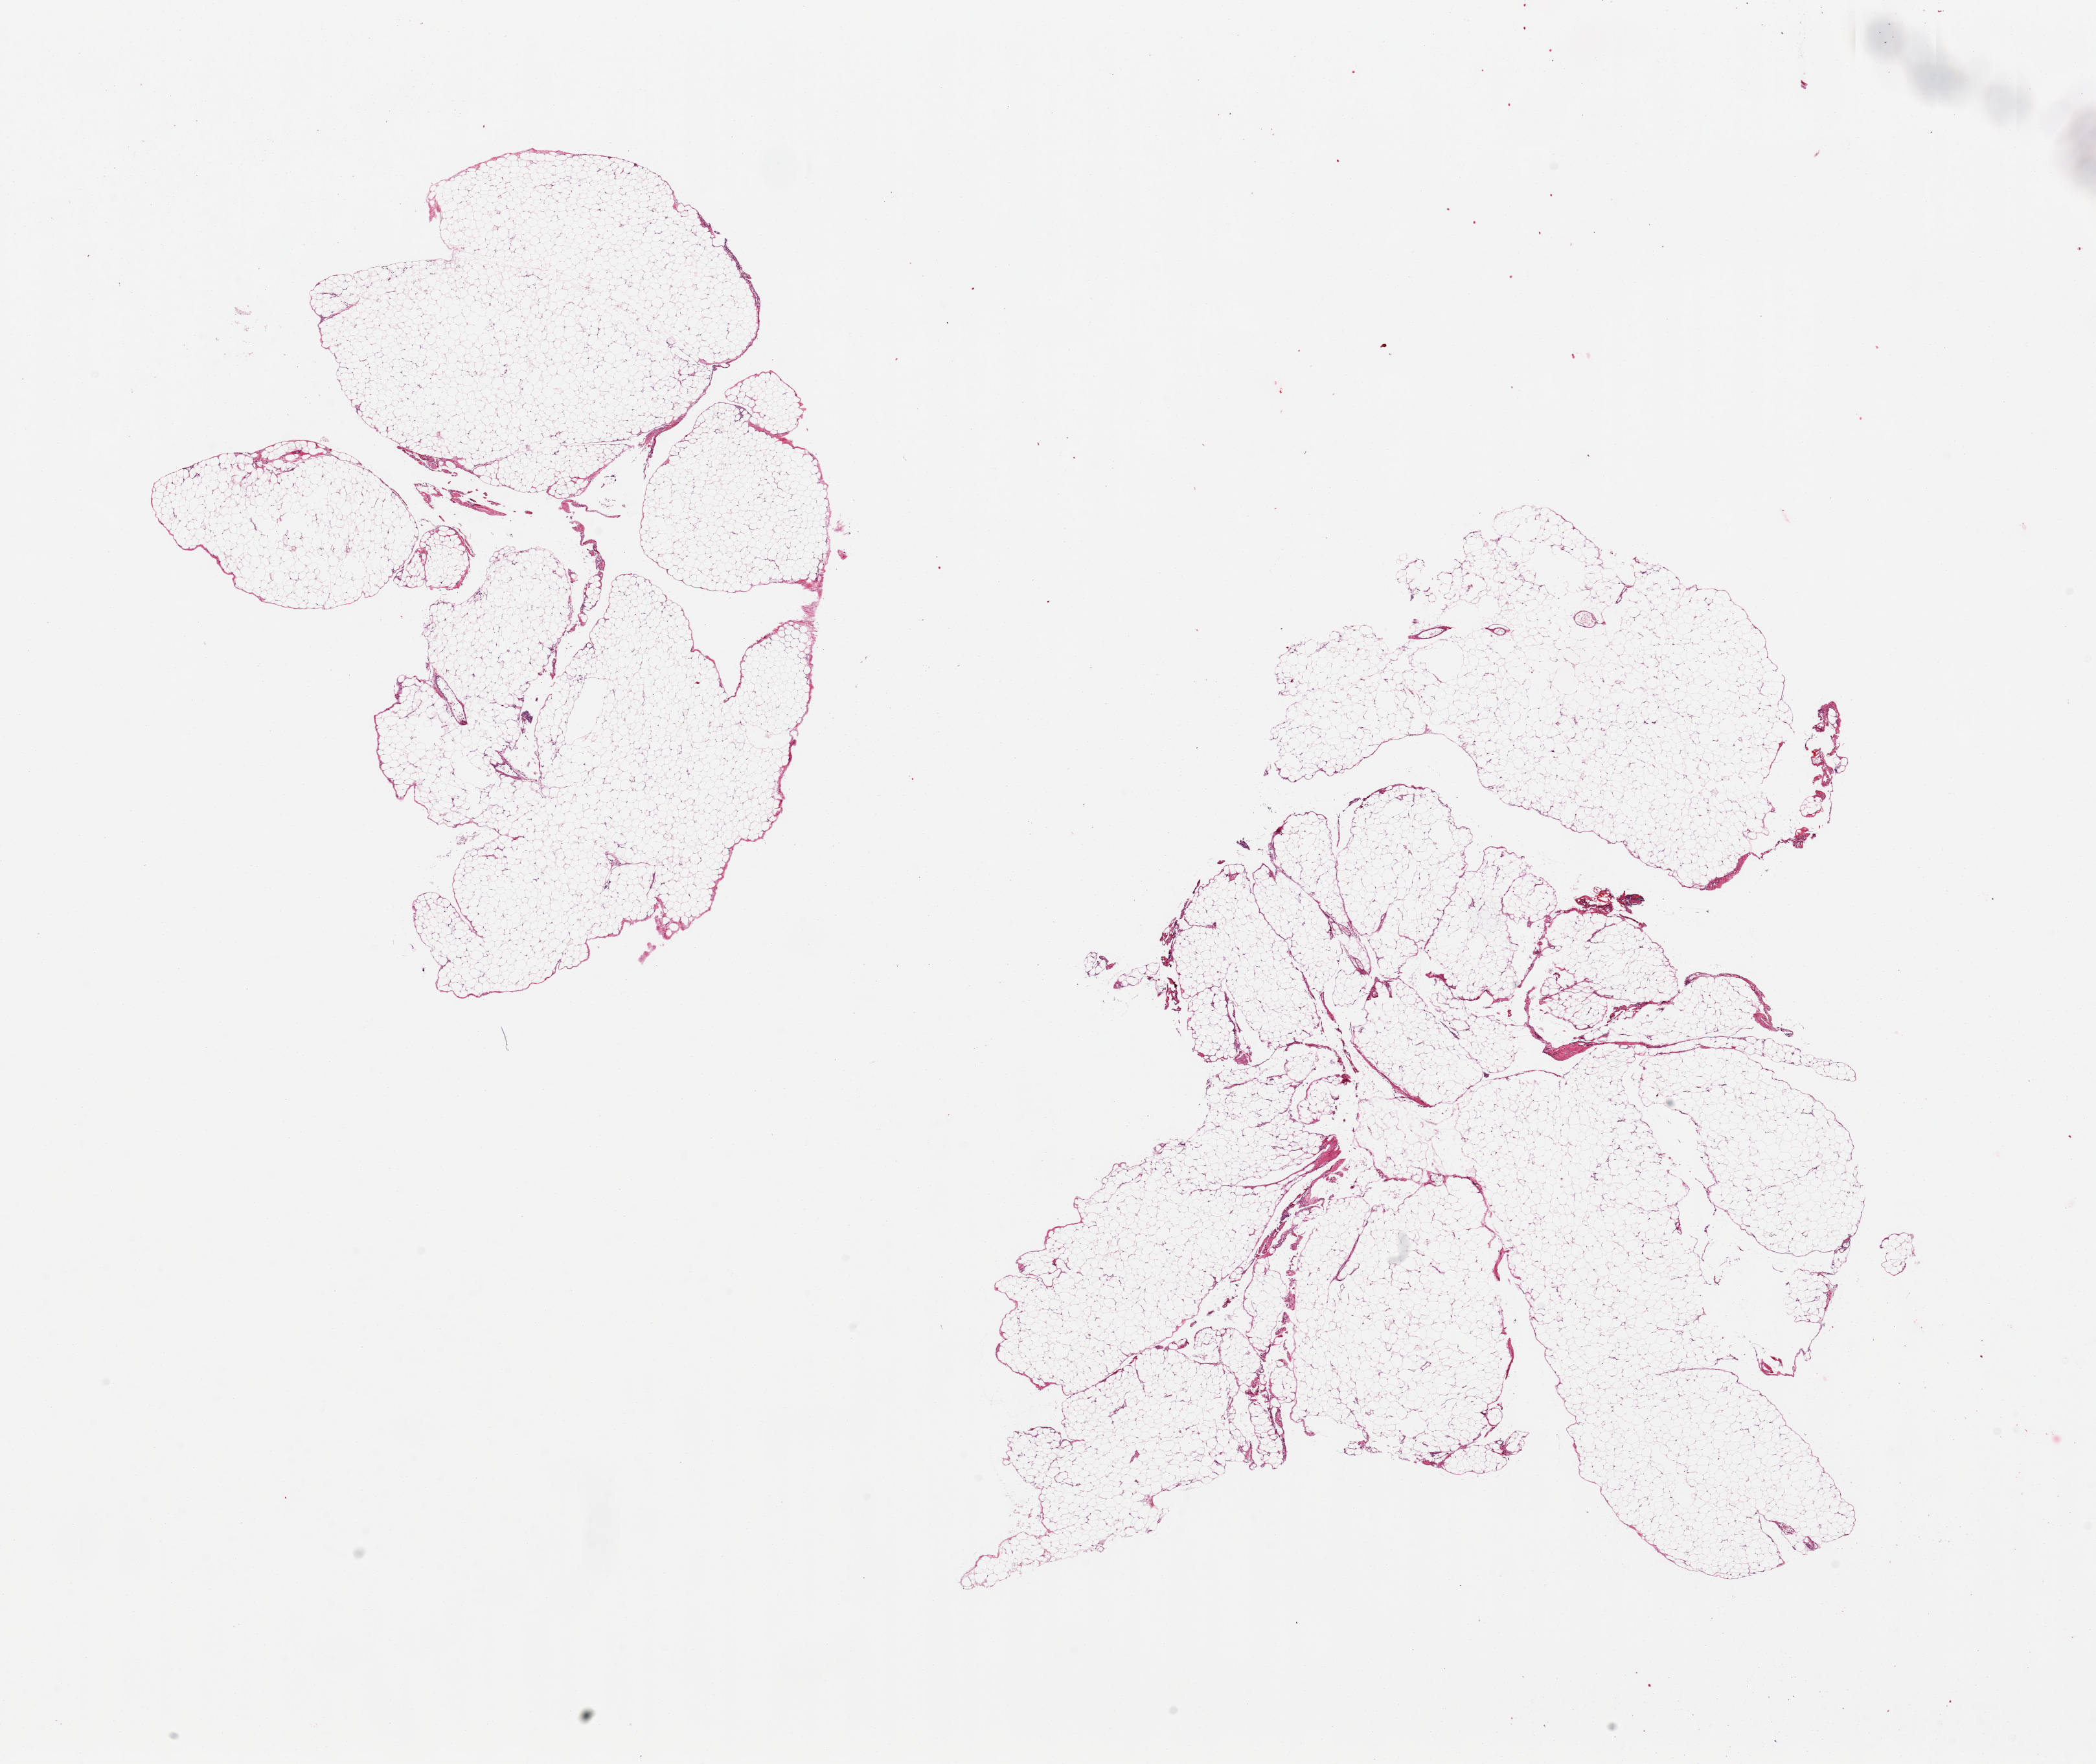
Whole-slide image, haematoxylin and eosin stain, brightfield — low-resolution overview of the scanned area, about 25.6 x 21.5 mm (from a 20x scan), PAXgene-fixed paraffin-embedded (PFPE) section, section of omentum (target tissue), donor tissue sample. Donor sex: male.
Review note (as recorded): 2 pieces.